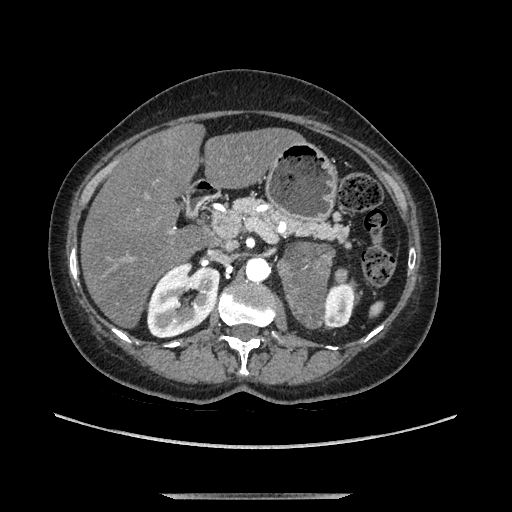
Contrast-enhanced abdominal CT, one axial slice; slice 66 of 169 in the series (ordered by position); soft-tissue window (W 400 / L 40 HU); 1.25 mm slice thickness; 512 × 512 image matrix. Female patient. Case-level facts recorded for this patient, not image findings: diagnosis: adrenocortical carcinoma; tumour side: left adrenal; tumour size at pathology: 9 cm; Ki-67 index: 2 %; stage (as recorded): 3.
Structures marked on this image (semi-automatic segmentation, software-assisted and operator-edited):
- mass: bounding box <283,245,332,327> (left, top, right, bottom; pixels)